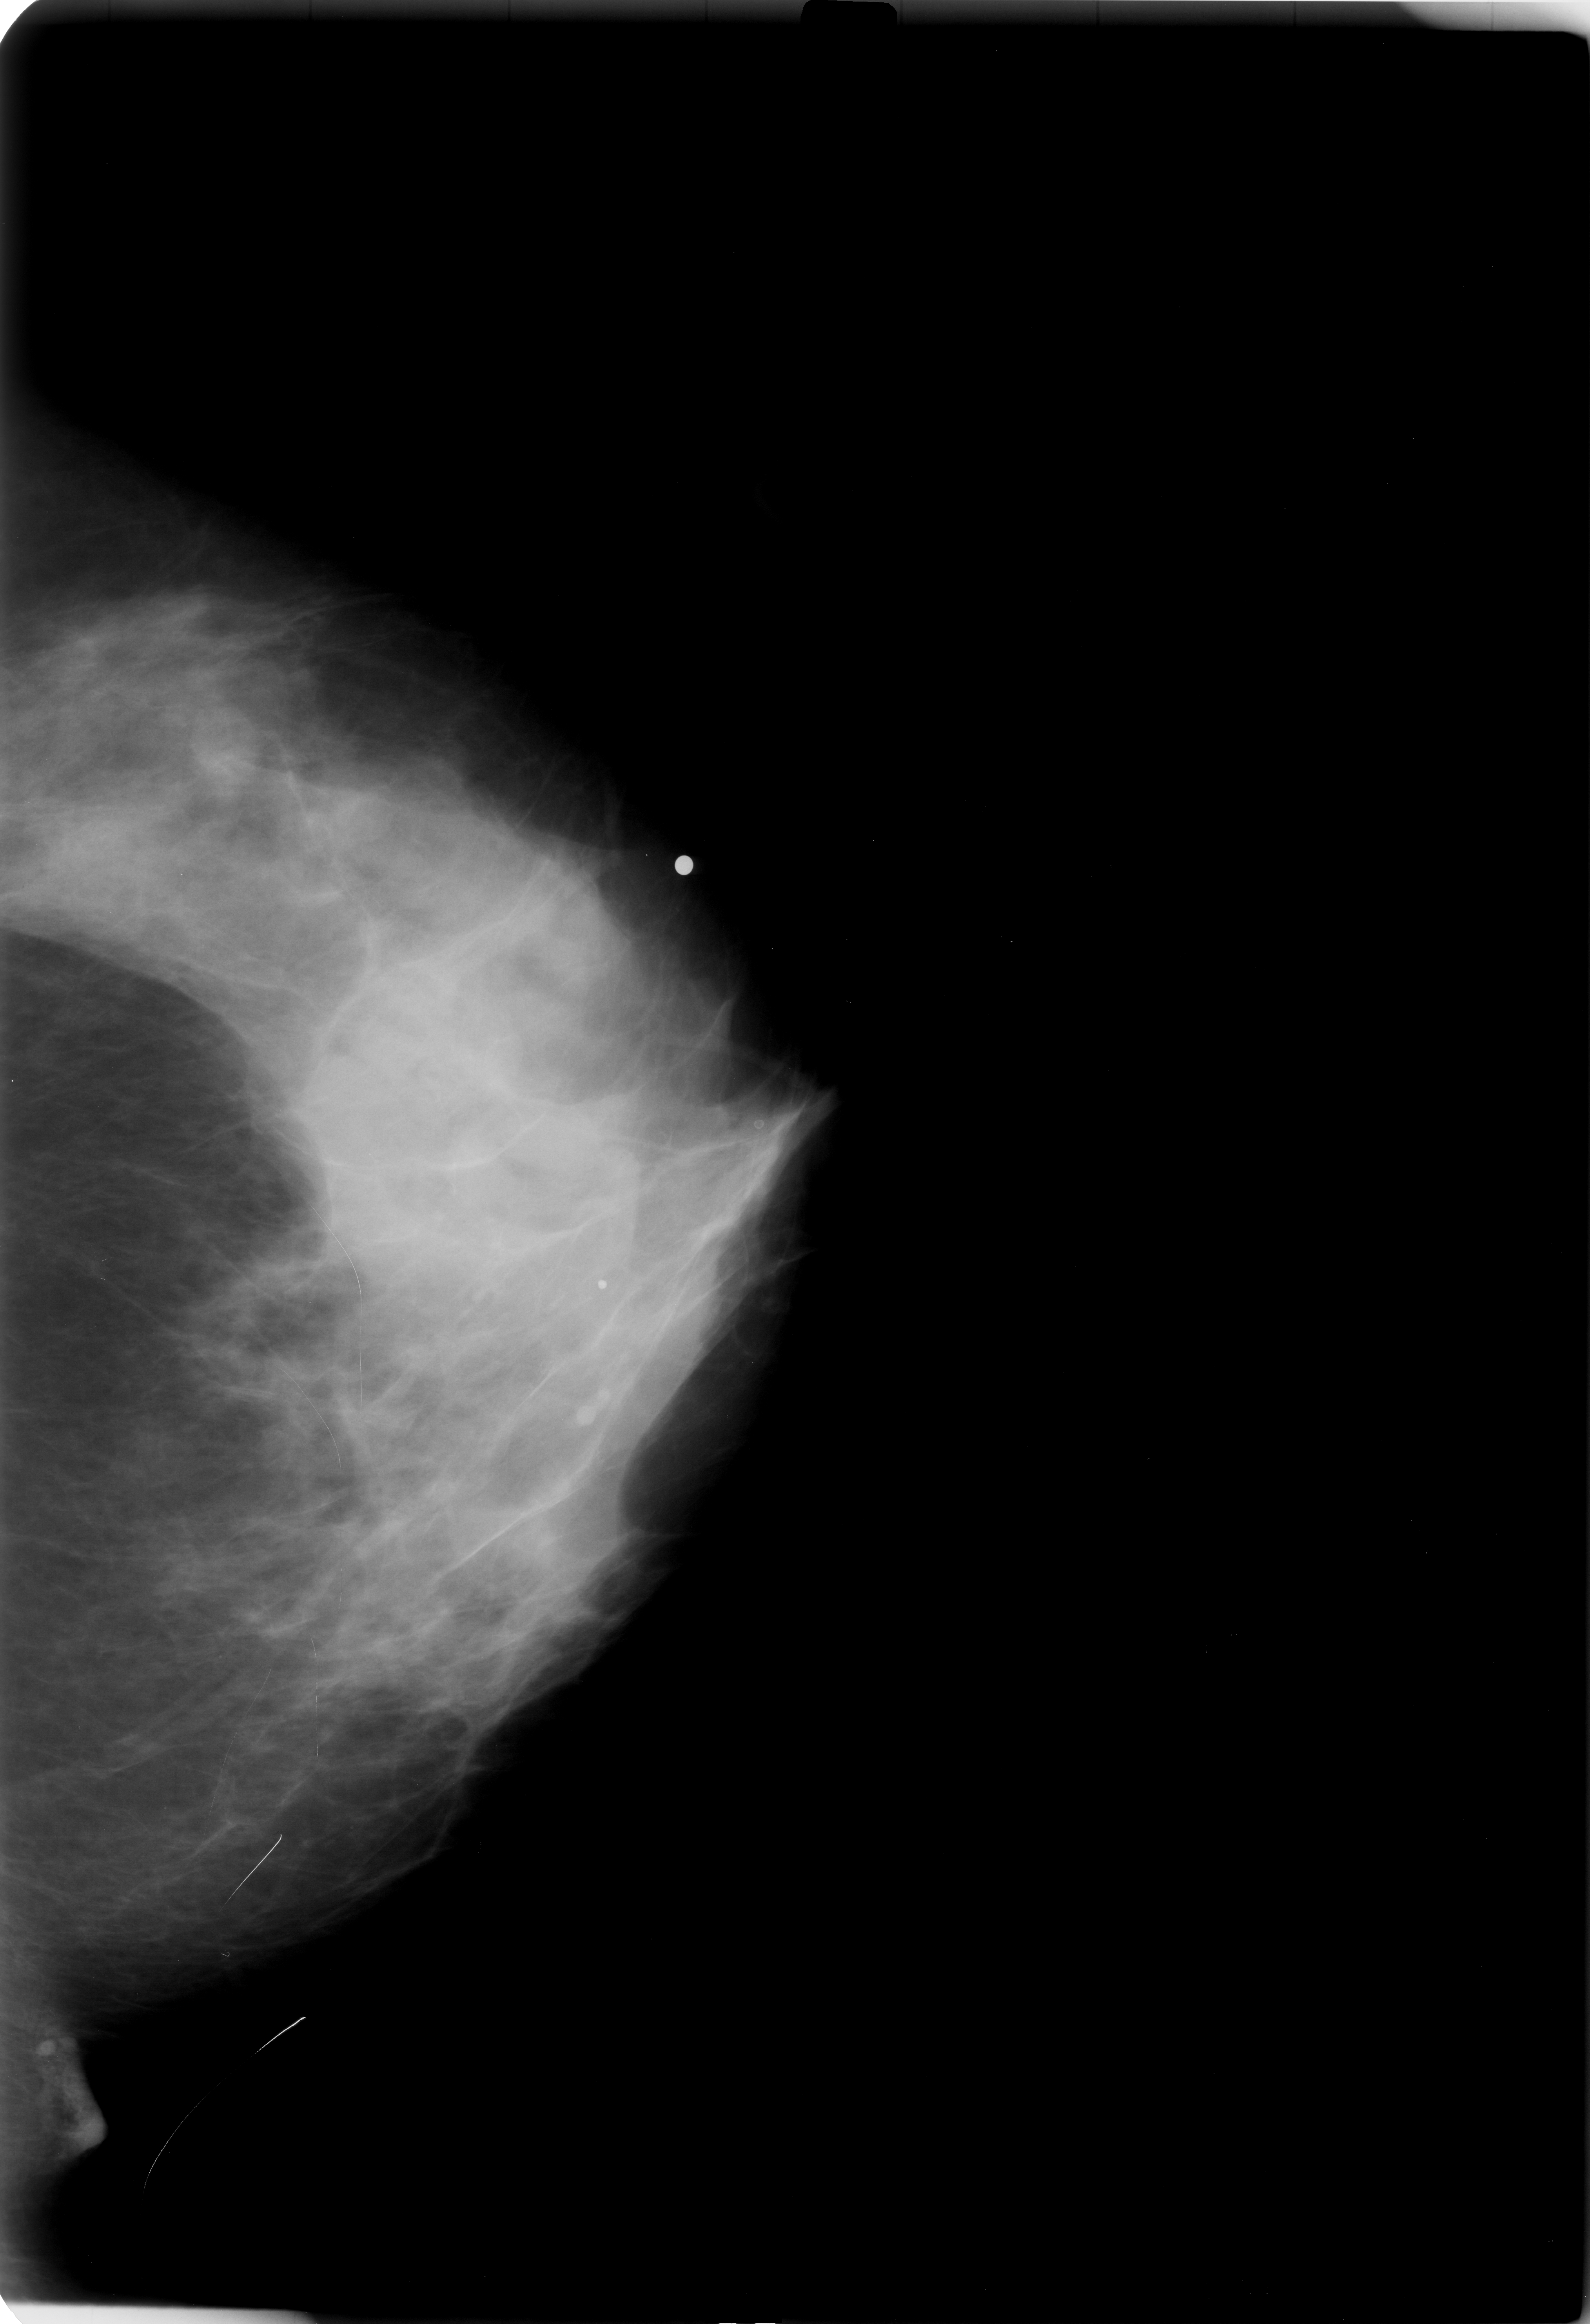
Digitized screen-film mammogram. Left breast. Craniocaudal (CC) view. BI-RADS breast density category 4 (scale 1–4). 1590 × 2324 image matrix.
Expert-marked regions of interest on this film, with their recorded descriptors:
- mass, shape focal asymmetric density; BI-RADS assessment category 3; subtlety rating 1 on a 1 (subtle) to 5 (obvious) scale; pathology (as recorded): malignant: bounding box (x1, y1, x2, y2) in pixels: (336, 1025, 539, 1228)